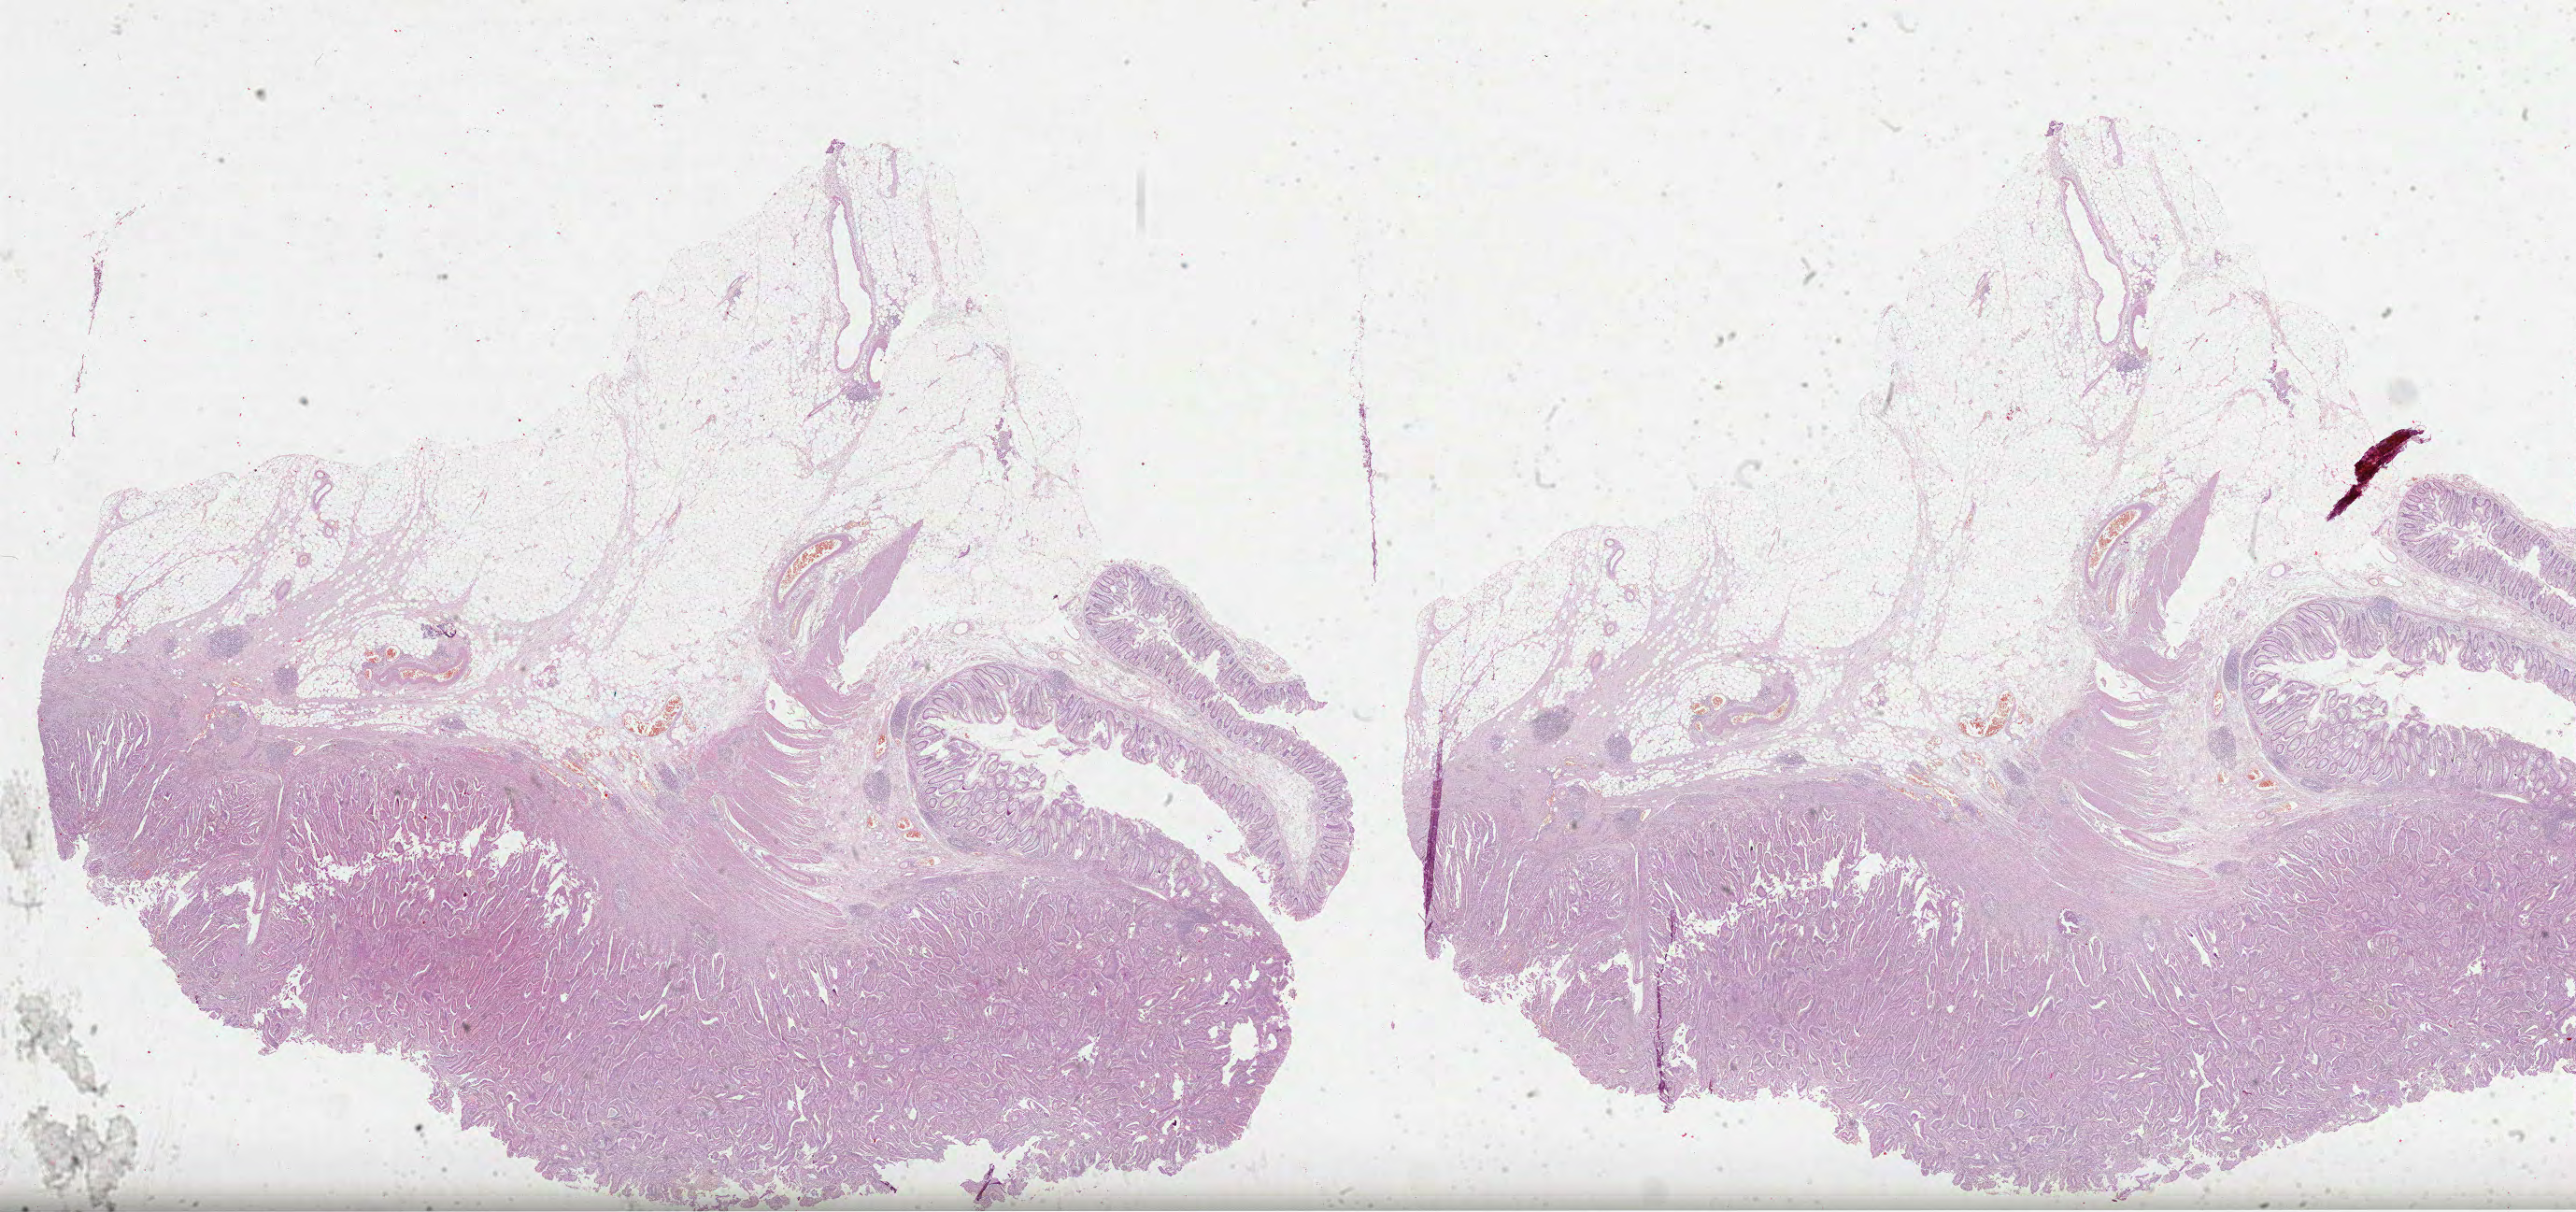
Whole-slide histology image, H&E — whole scanned area (about 44.5 x 20.9 mm, acquisition: 40x scan) shown as a low-resolution overview, formalin-fixed paraffin-embedded (FFPE) diagnostic section, primary tumour sample from the colon. Male patient; age at initial diagnosis 53 years.
TNM: T2 N0 M0. Pathologic diagnosis: Adenocarcinoma, NOS (cecum). AJCC pathologic stage: I. Lymph nodes positive (case pathology): 0 of 15 examined.